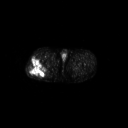
FDG PET of an extremity soft-tissue mass (from a PET/CT study), one axial slice; slice 257 of 267 in the series (ordered by position); 3.27 mm slice thickness; 128 × 128 image matrix, field of view 700 × 700 mm. Patient: male, 43 years. From the clinical record (not read from this slice): histological type: poorly differentiated synovial sarcoma; grade: high; site of the primary tumour: right buttock.
Structures marked on this image (expert contour drawn on MRI and transferred to this co-registered scan by the dataset authors):
- gross tumour volume including surrounding oedema: bounding box <27,57,47,78> (left, top, right, bottom; pixels)
- gross tumour volume (mass): <27,57,47,78>